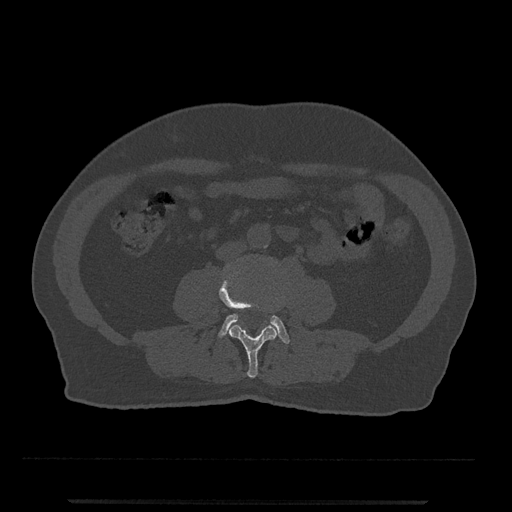
CT including the spine, one axial slice; slice 176 of 797 in the series (ordered by position); 120 kVp; bone window (W 1800 / L 400 HU); 0.5 mm slice thickness; 512 × 512 image matrix. Patient: male, 63 years. From the clinical record (not read from this slice): primary cancer: prostate.
Structures marked on this image (semi-automatically segmented with operator editing):
- L3 vertebra: bounding box [x1, y1, x2, y2] px = [219, 269, 277, 378]
- L4 vertebra: [218, 314, 290, 344]